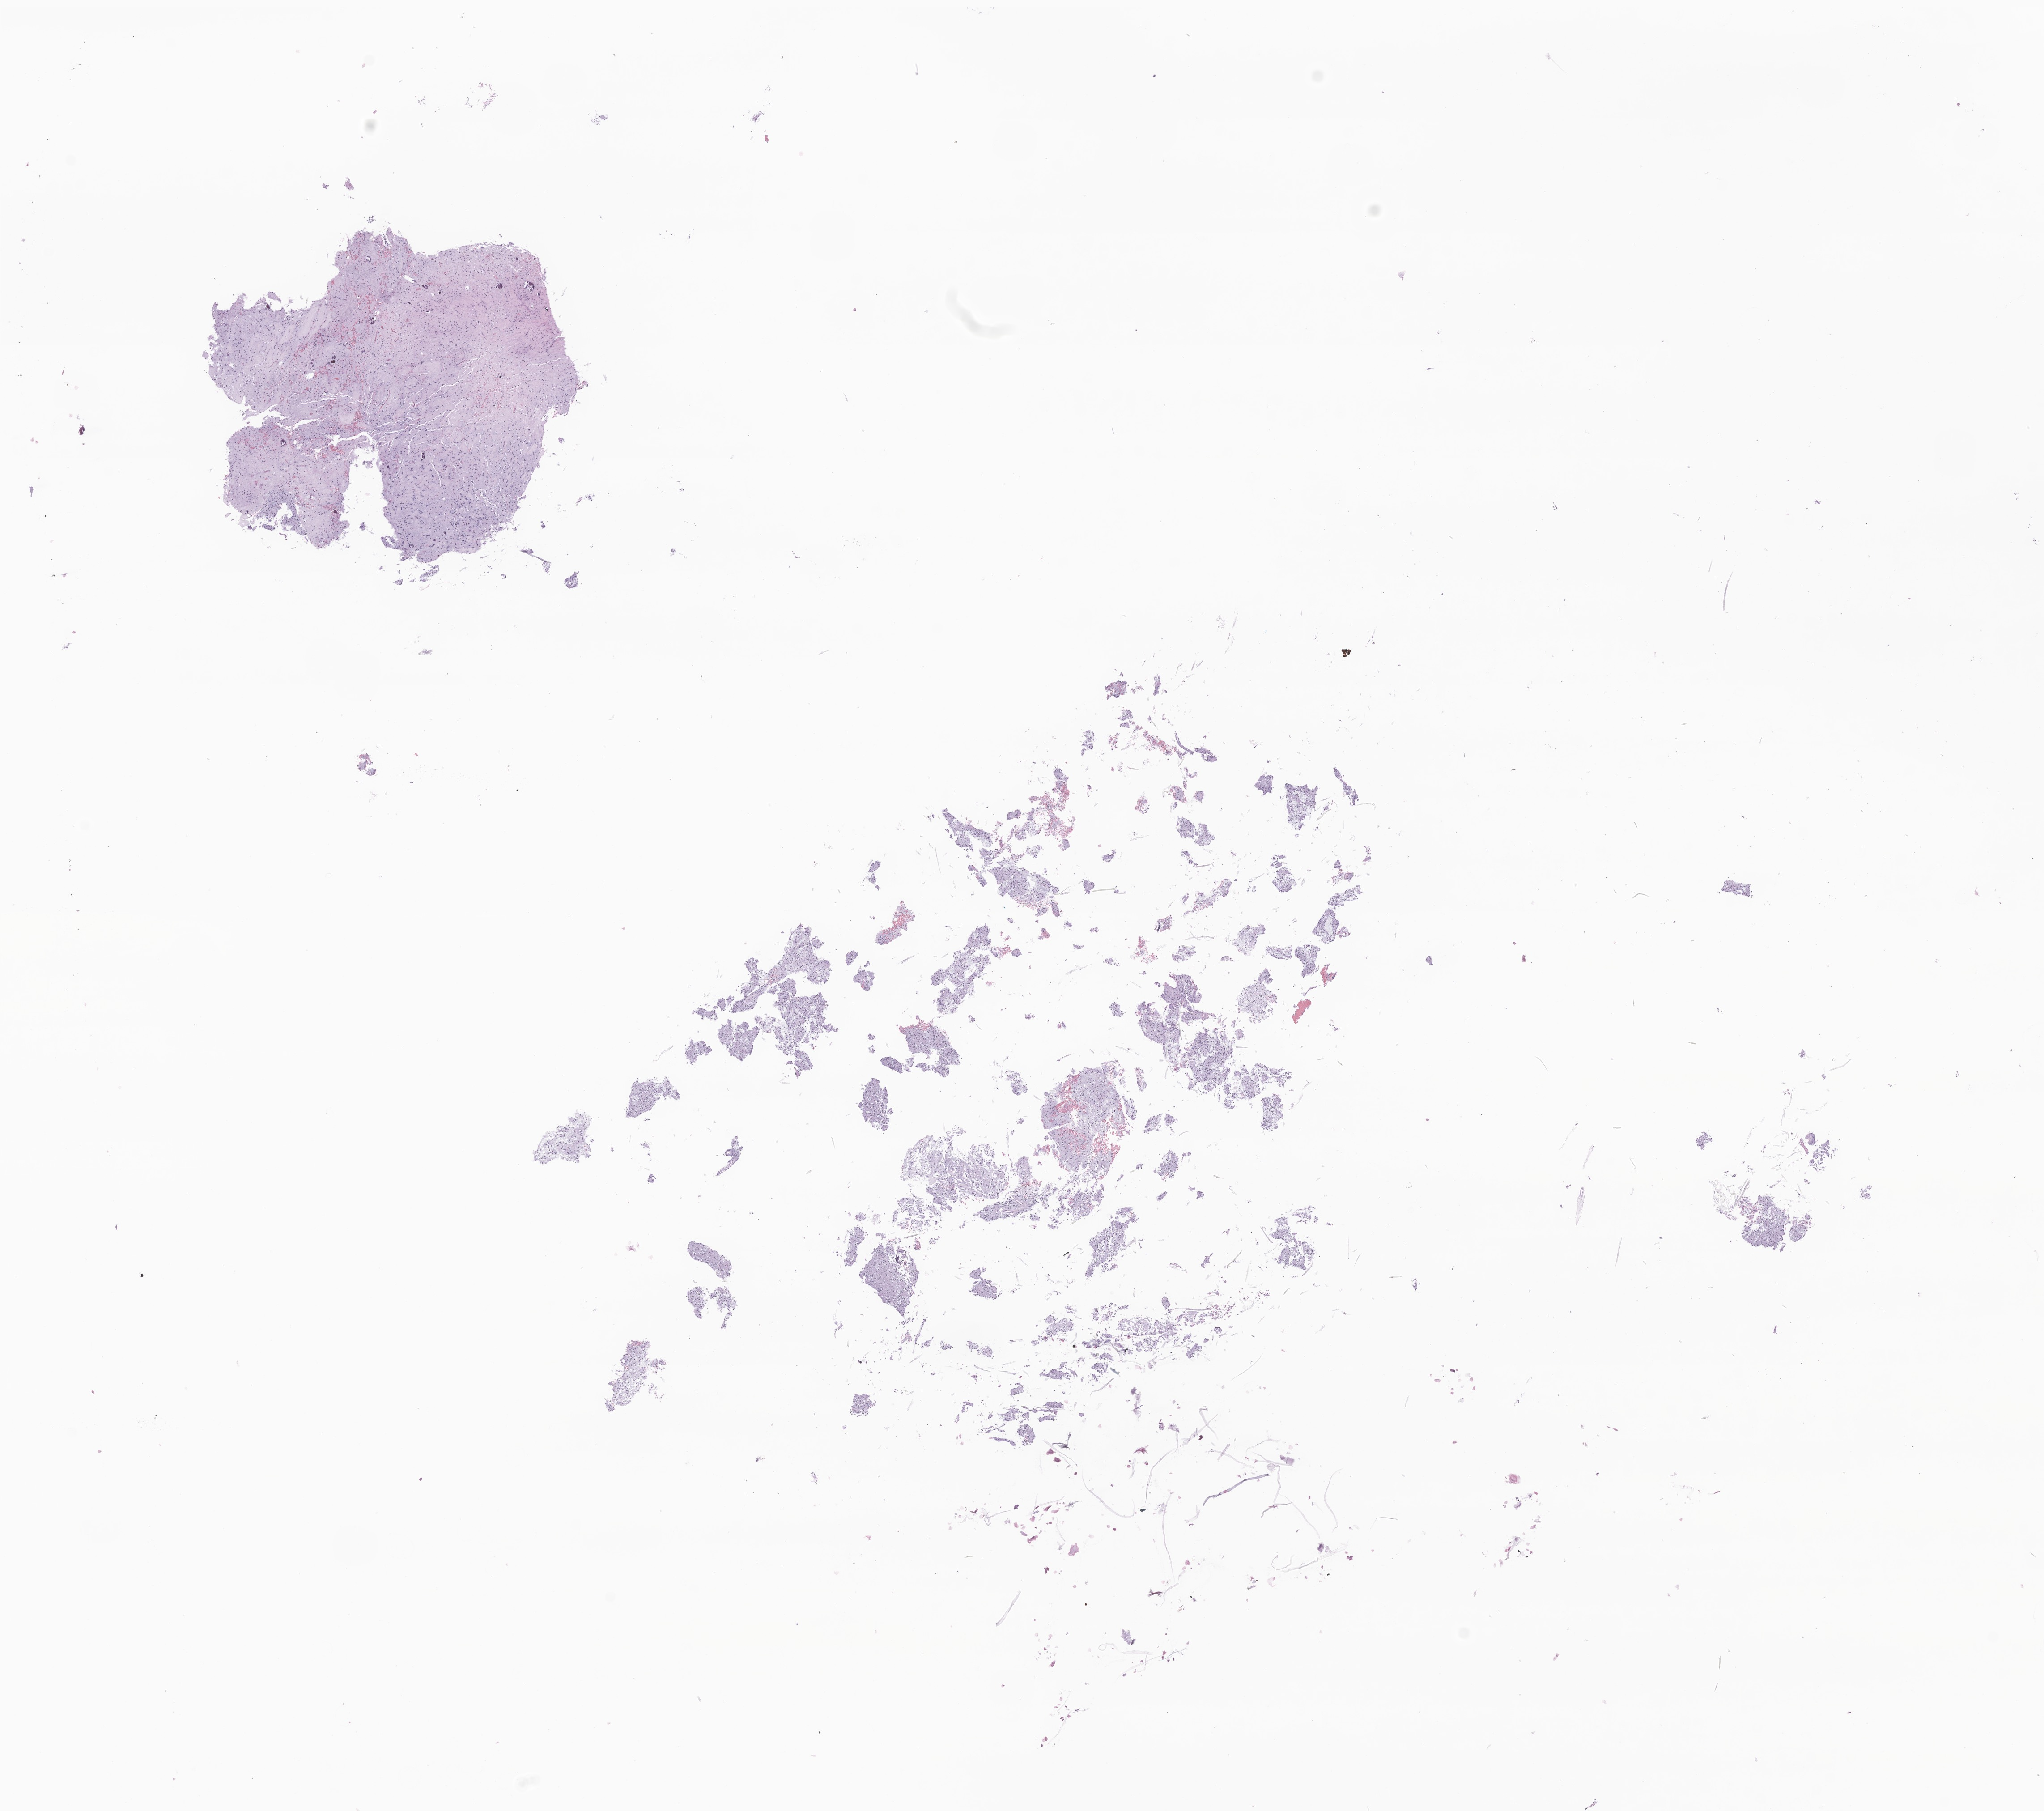
Hematoxylin and eosin (H&E) whole-slide image of tumor tissue from the brain, shown as a low-resolution overview of the whole scanned area (about 19.3 x 17.1 mm). Formalin-fixed, paraffin-embedded (FFPE) tissue. Patient male; age 215 months.
Diagnosis (ICD-O-3 morphology term): Glioma, malignant.